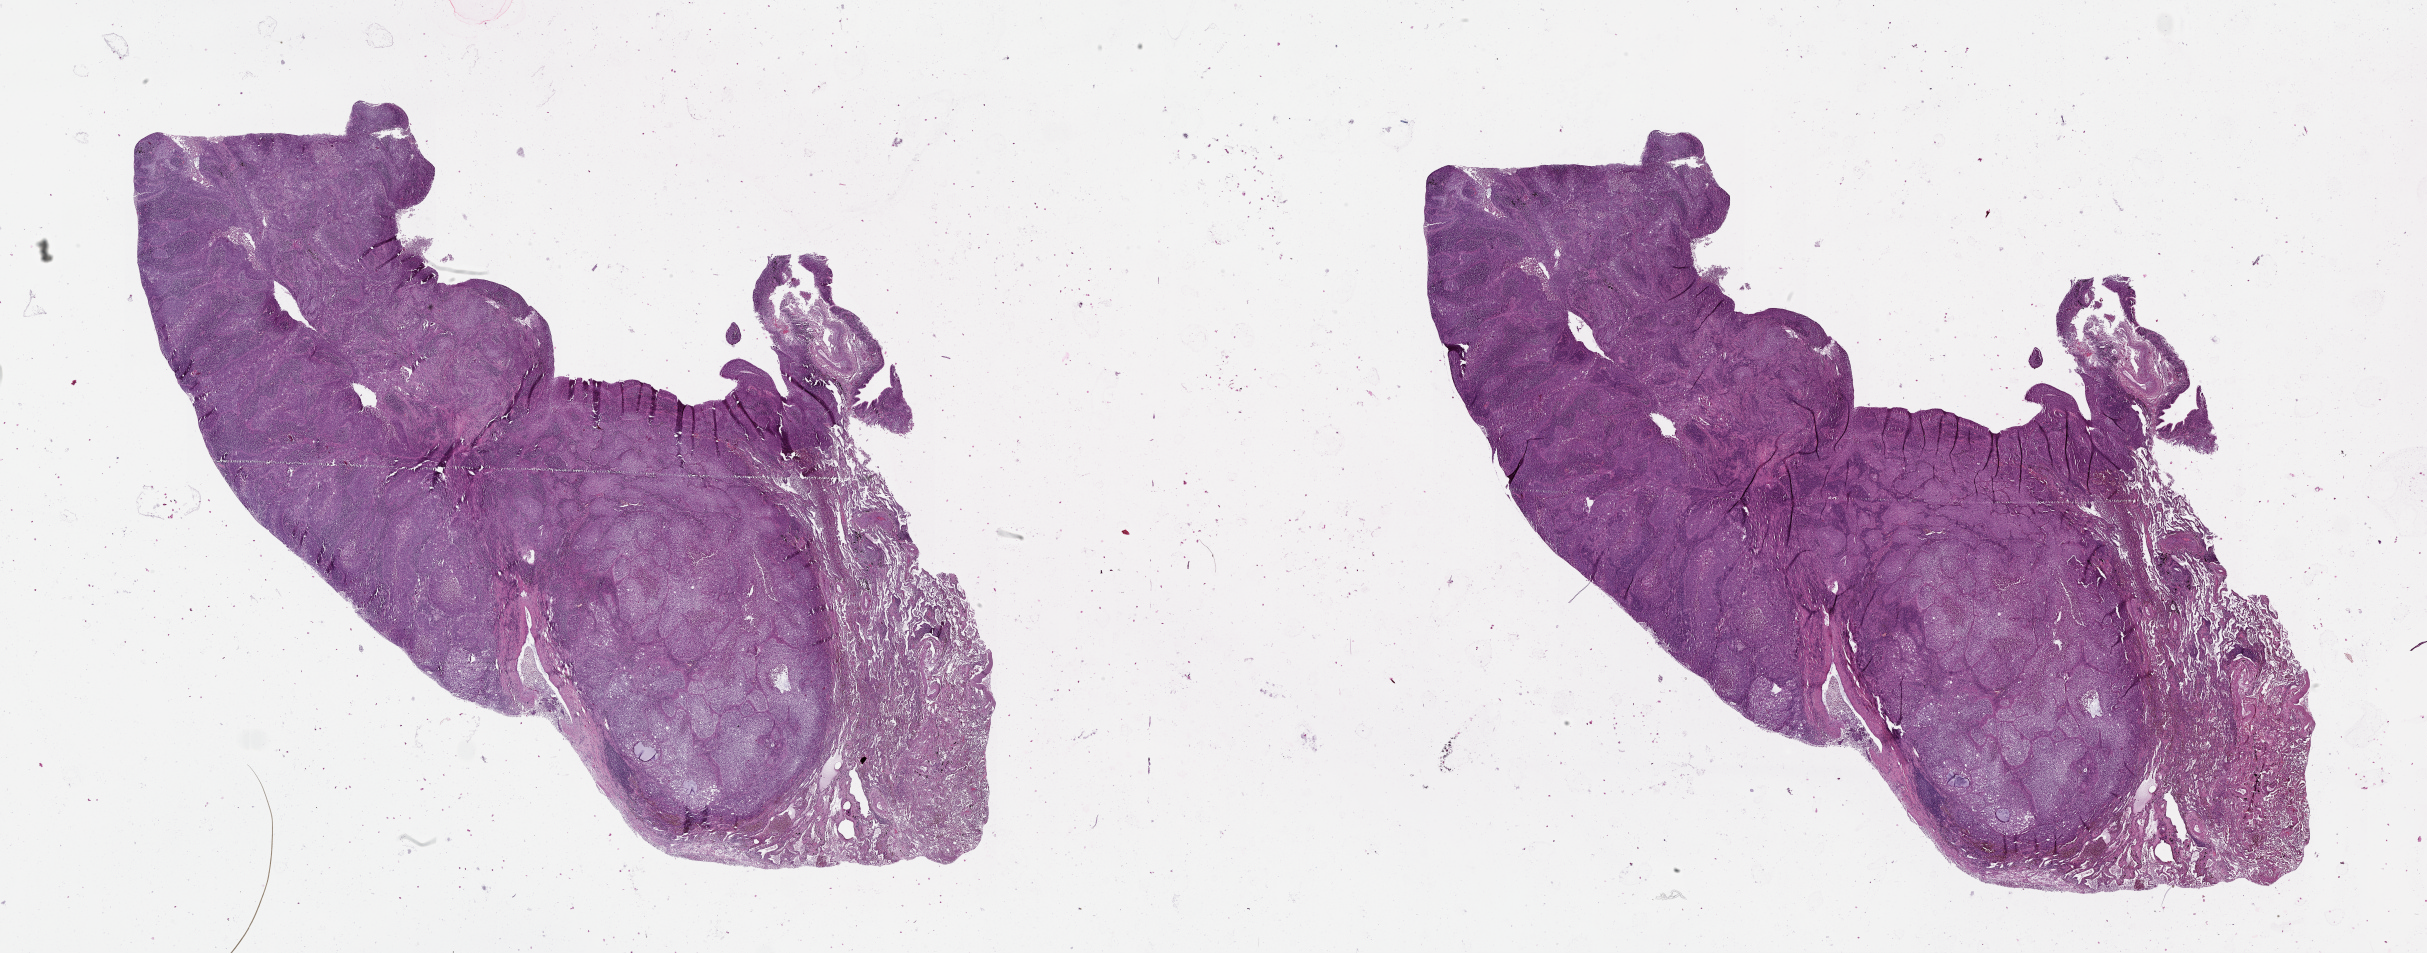
Whole-slide histology image, Hematoxylin and eosin (H&E) stained — low-resolution overview of the scanned area, about 39.1 x 15.3 mm, lung, tumour tissue. 72-year-old female patient.
Patient diagnosis (cohort enrolment): squamous cell carcinoma (lung).